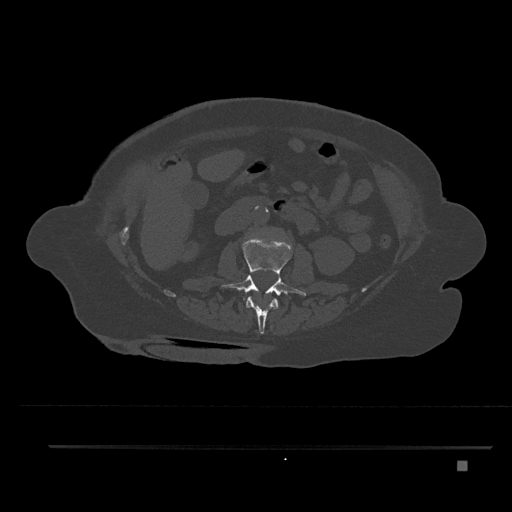
CT including the spine, one axial slice. Slice 177 of 797 in the series (ordered by position). Reconstruction kernel Br40s/3. 120 kVp. Bone window (W 1800 / L 400 HU). 0.5 mm slice thickness. 512 × 512 image matrix, field of view 437 × 437 mm. Patient: female, 76 years. From the clinical record (not read from this slice): primary cancer: lung; vertebrae with lytic lesions (as recorded): T11, L3.
Annotated regions visible in this slice (semi-automatically segmented with operator editing):
- L1 vertebra: bounding box <246,296,279,334> (left, top, right, bottom; pixels)
- L2 vertebra: <221,237,306,303>